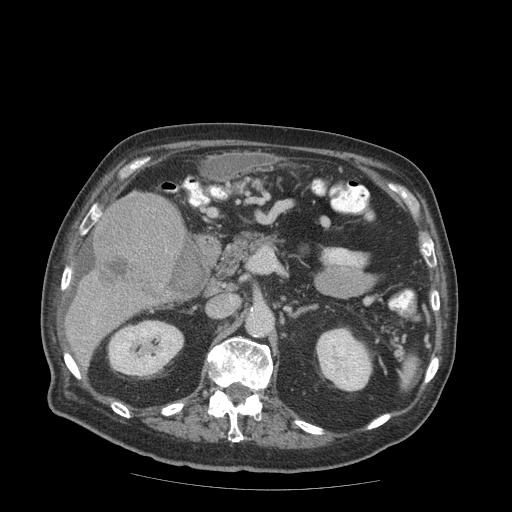
Contrast-enhanced abdominal CT (liver protocol), one axial slice; position 35 of 99 along the scan axis; reconstruction kernel STANDARD; soft-tissue window (W 400 / L 40 HU); 2.5 mm slice thickness; 512 × 512 image matrix, field of view 420 × 420 mm. Case-level facts recorded for this patient, not image findings: diagnosis: hepatocellular carcinoma (patient treated with transarterial chemoembolisation; whether this scan precedes or follows treatment is not stated here); TNM stage (as recorded): Stage-IIIB; Child-Pugh class: A; tumour differentiation: well differentiated; tumour nodularity: multinodular.
Outlined on this slice (semi-automatic segmentation, software-assisted and operator-edited):
- liver parenchyma outside the tumour (the mass and vessels are separate outlines, so this box may not span the whole liver): bounding box <64,194,186,356> (left, top, right, bottom; pixels)
- mass: <90,190,186,305>